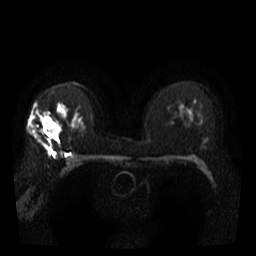
Breast MRI, one axial slice. Position 24 of 40 along the scan axis. Diffusion-weighted series; image 2 of 4 stored at this slice position (different b-values; order by instance number). 3 T. 5 mm slice thickness. 256 × 256 image matrix, field of view 300 × 300 mm. Female patient.
Outlined on this slice (expert manual segmentation):
- tumour on diffusion-weighted imaging: bounding box [x1, y1, x2, y2] px = [44, 116, 62, 137]